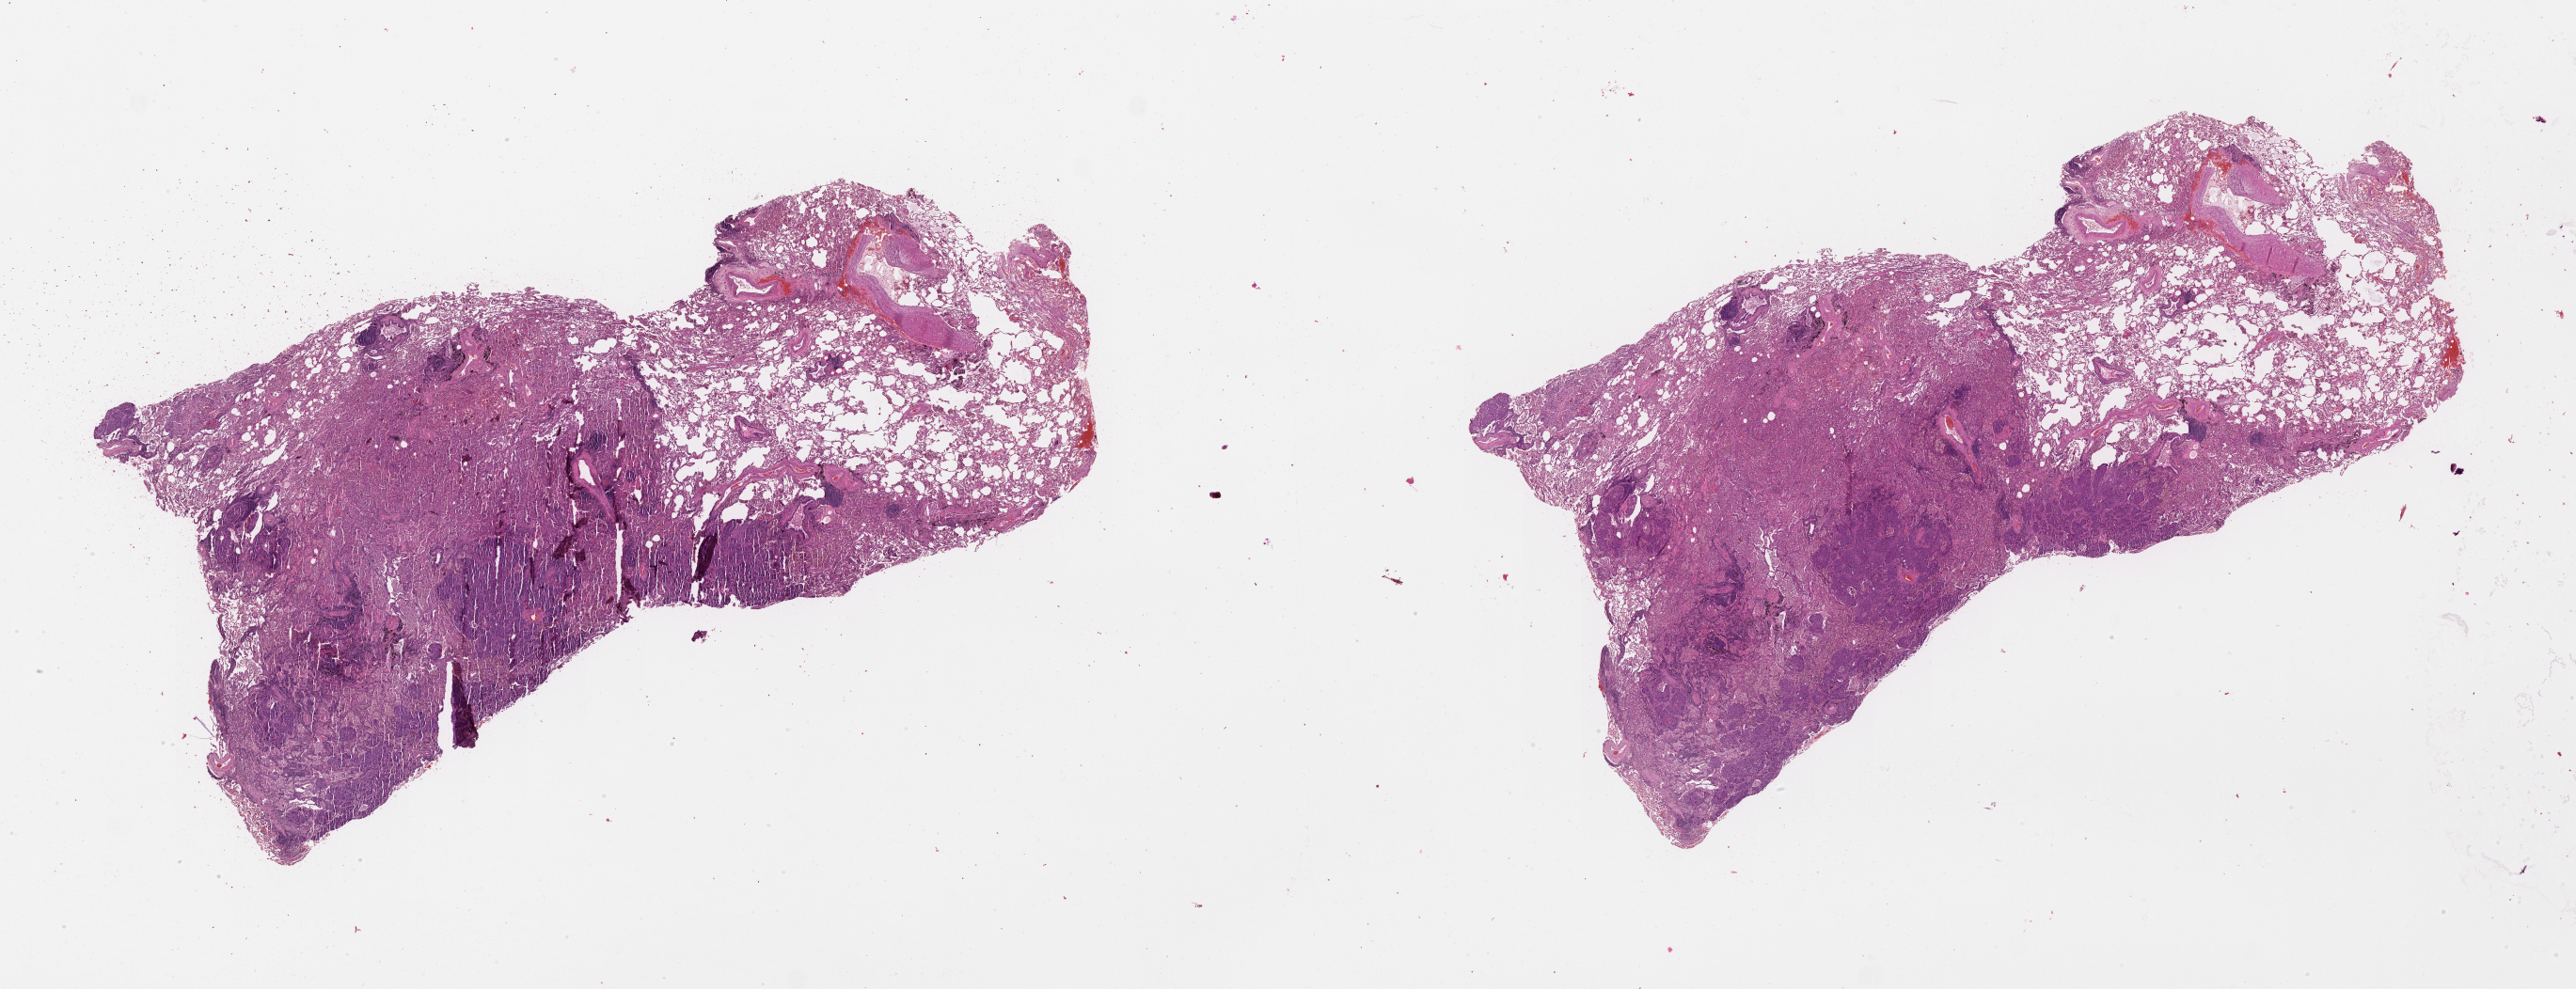
Digitized Hematoxylin and eosin (H&E) stained tissue section (whole slide) — low-resolution overview of the scanned area, about 44.1 x 16.9 mm (acquisition: 20x scan); lung, tumour tissue. Male, 59 y/o.
Patient diagnosis (cohort enrolment): squamous cell carcinoma (lung).